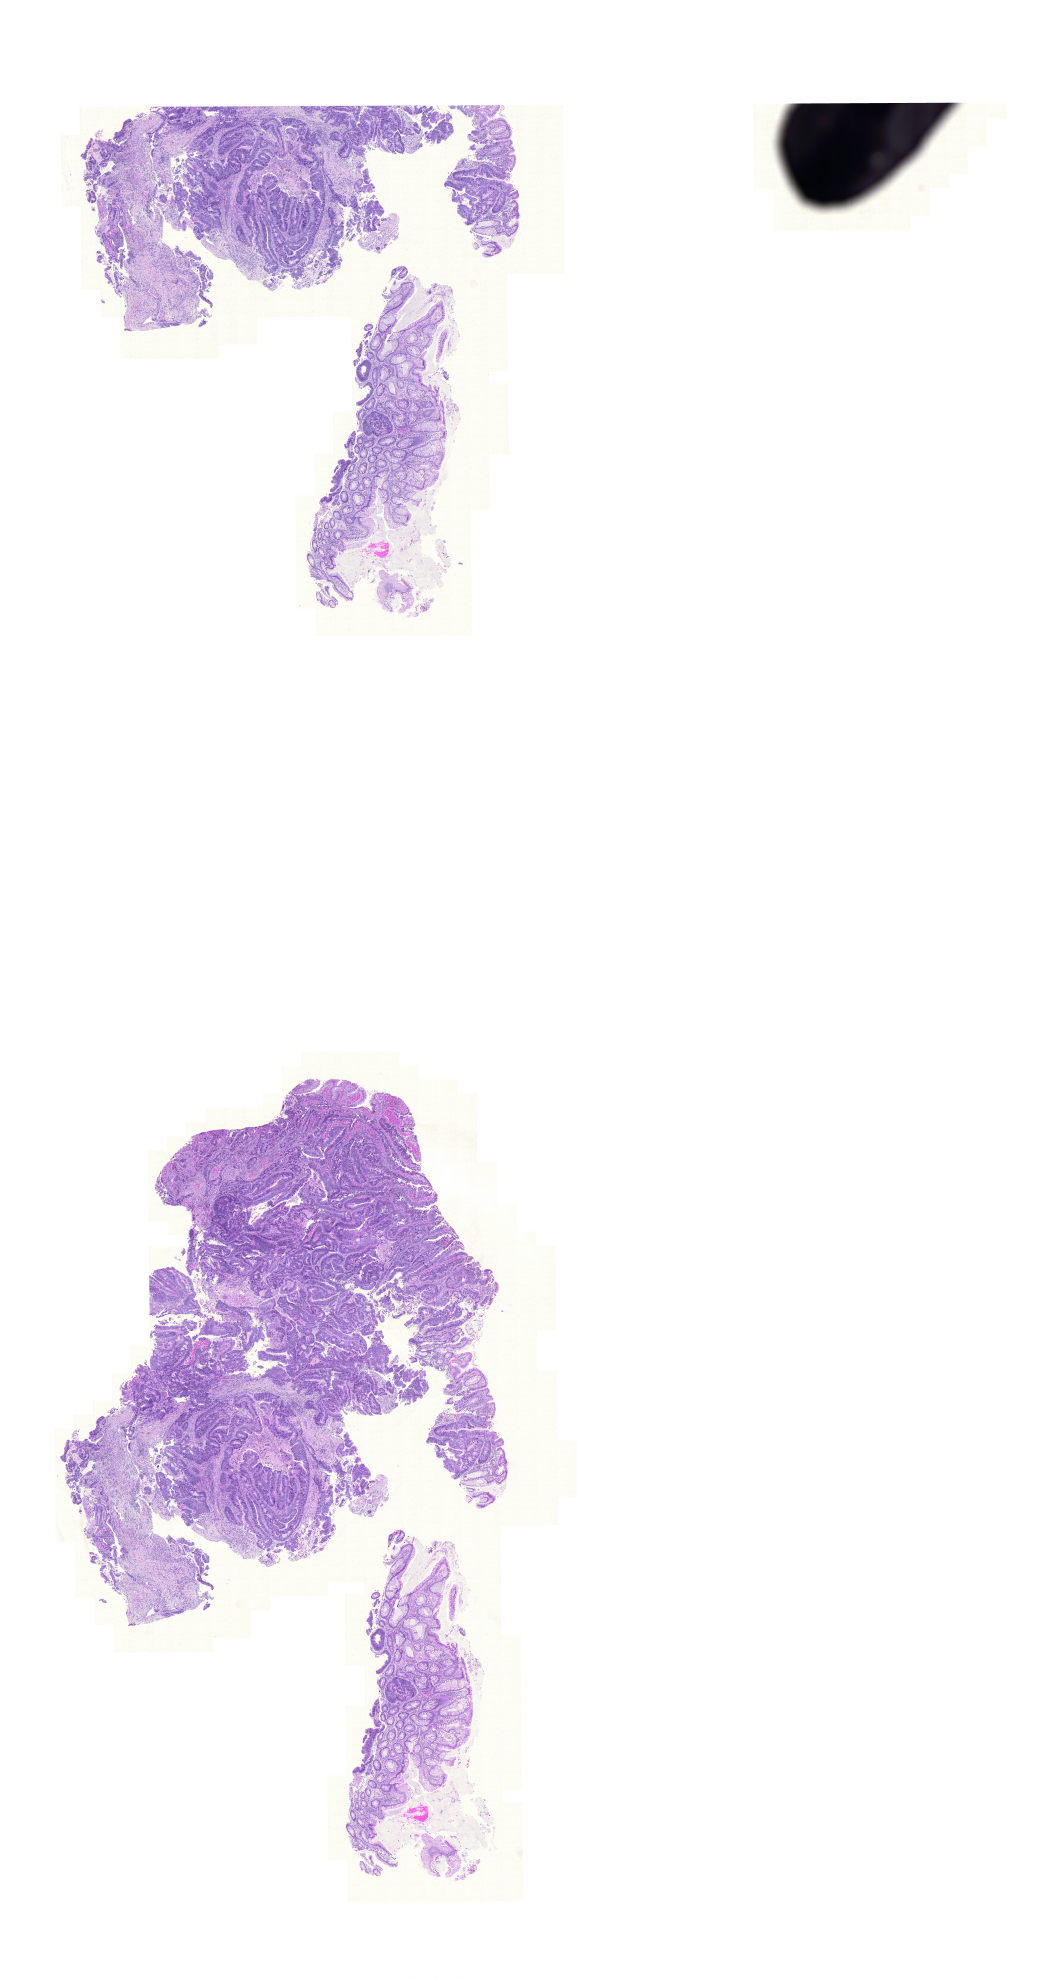
Digitized H&E tissue section (whole slide), a low-resolution overview of the entire scanned area, about 15.5 x 29.5 mm; formalin-fixed paraffin-embedded (FFPE) diagnostic section; rectum, primary tumour sample. Male, age 75 years at initial diagnosis.
AJCC pathologic stage: IIA (6th edition). Lymph nodes positive (case pathology): 0 of 32 examined. Pathologic diagnosis: Adenocarcinoma, NOS.